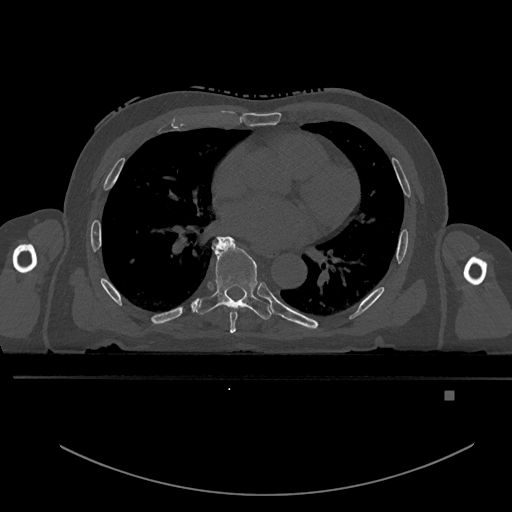
CT including the spine, one axial slice; slice 268 of 969 in the series (ordered by position); bone window (W 1800 / L 400 HU); 0.5 mm slice thickness; 512 × 512 image matrix, field of view 456 × 456 mm. Patient: male, 82 years. Case-level facts recorded for this patient, not image findings: primary cancer: prostate.
Annotated regions visible in this slice (semi-automatic segmentation, software-assisted and operator-edited):
- T6 vertebra: box from (x=230, y=309) to (x=238, y=333) px
- T7 vertebra: (x=193, y=236)–(x=272, y=320)